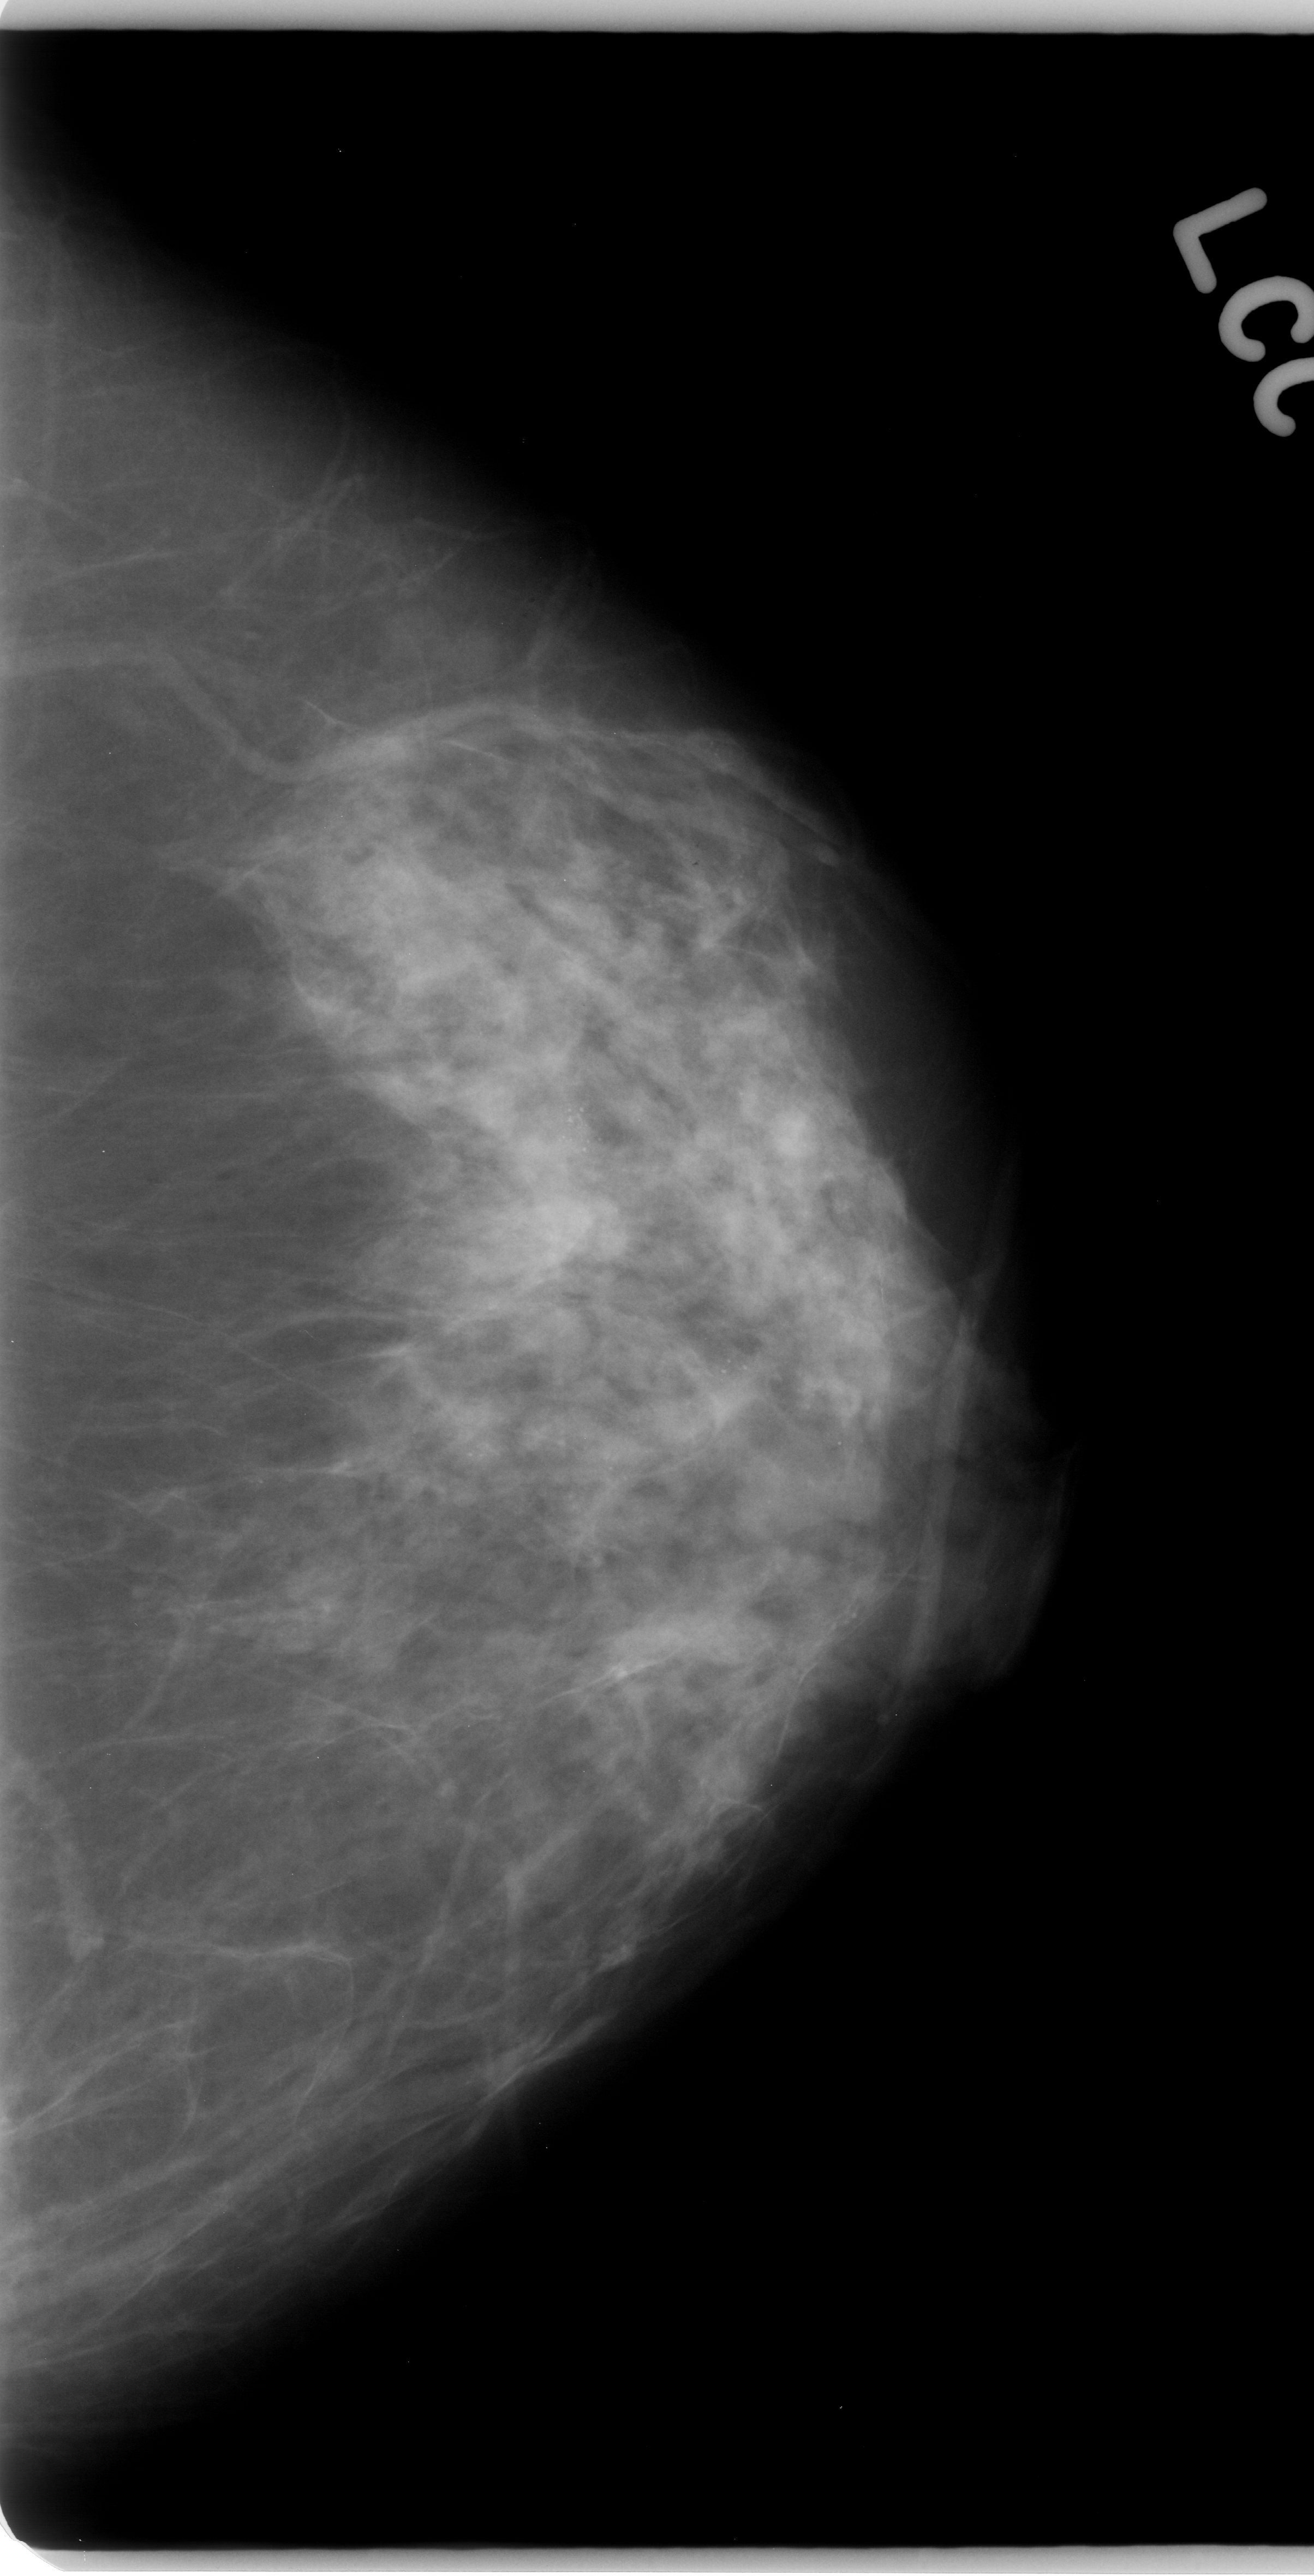
Mammogram (digitized film); left breast; CC view; breast composition: scattered fibroglandular densities (BI-RADS density category 2 of 4).
Abnormality record for this image: calcifications, morphology amorphous, distribution regional; BI-RADS assessment category 4; subtlety rating 3 on a 1 (subtle) to 5 (obvious) scale; pathology (as recorded): malignant.